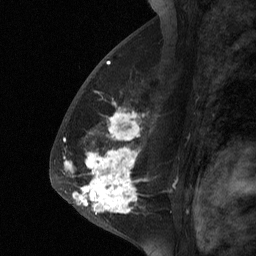
Breast MRI (dynamic contrast-enhanced), one sagittal slice; slice 38 of 64 in the series (ordered by position); dynamic contrast-enhanced study with each time point stored as its own series, time point 2 of 3 at this slice position (early post-contrast, ordered by acquisition time); 1.5 T; TE 4.8 ms, TR 27 ms; 2 mm slice thickness; 256 × 256 image matrix, field of view 180 × 180 mm. Female patient, age 56 years. Case-level facts recorded for this patient, not image findings: setting: breast cancer imaged before/during neoadjuvant chemotherapy; receptor status: HER2-positive.
Annotated regions visible in this slice (semi-automatic segmentation, software-assisted and operator-edited):
- analysis volume of interest (the breast-tissue region the enhancement analysis was run in; not a lesion): bounding box [x1, y1, x2, y2] px = [59, 104, 156, 229]
- tumour enhancement mask (voxels above the 90 % enhancement threshold inside the analysis volume of interest): [66, 124, 136, 213]